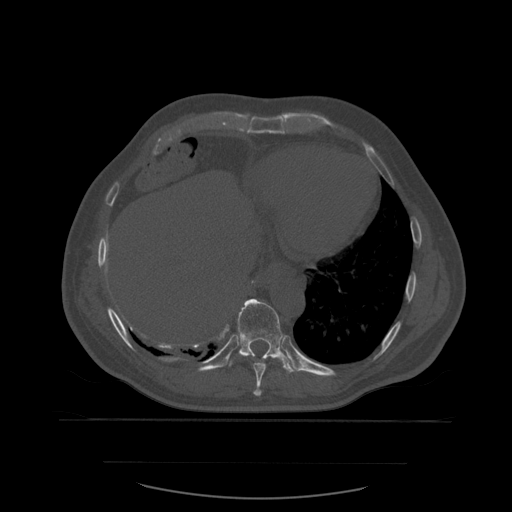
CT including the spine, one axial slice; position 328 of 590 along the scan axis; bone window (W 1800 / L 400 HU); 512 × 512 image matrix. Patient age 71 years. From the clinical record (not read from this slice): primary cancer: lung.
Outlined on this slice (semi-automatically segmented with operator editing):
- T10 vertebra: bounding box <228,299,299,374> (left, top, right, bottom; pixels)
- T9 vertebra: <254,358,267,397>